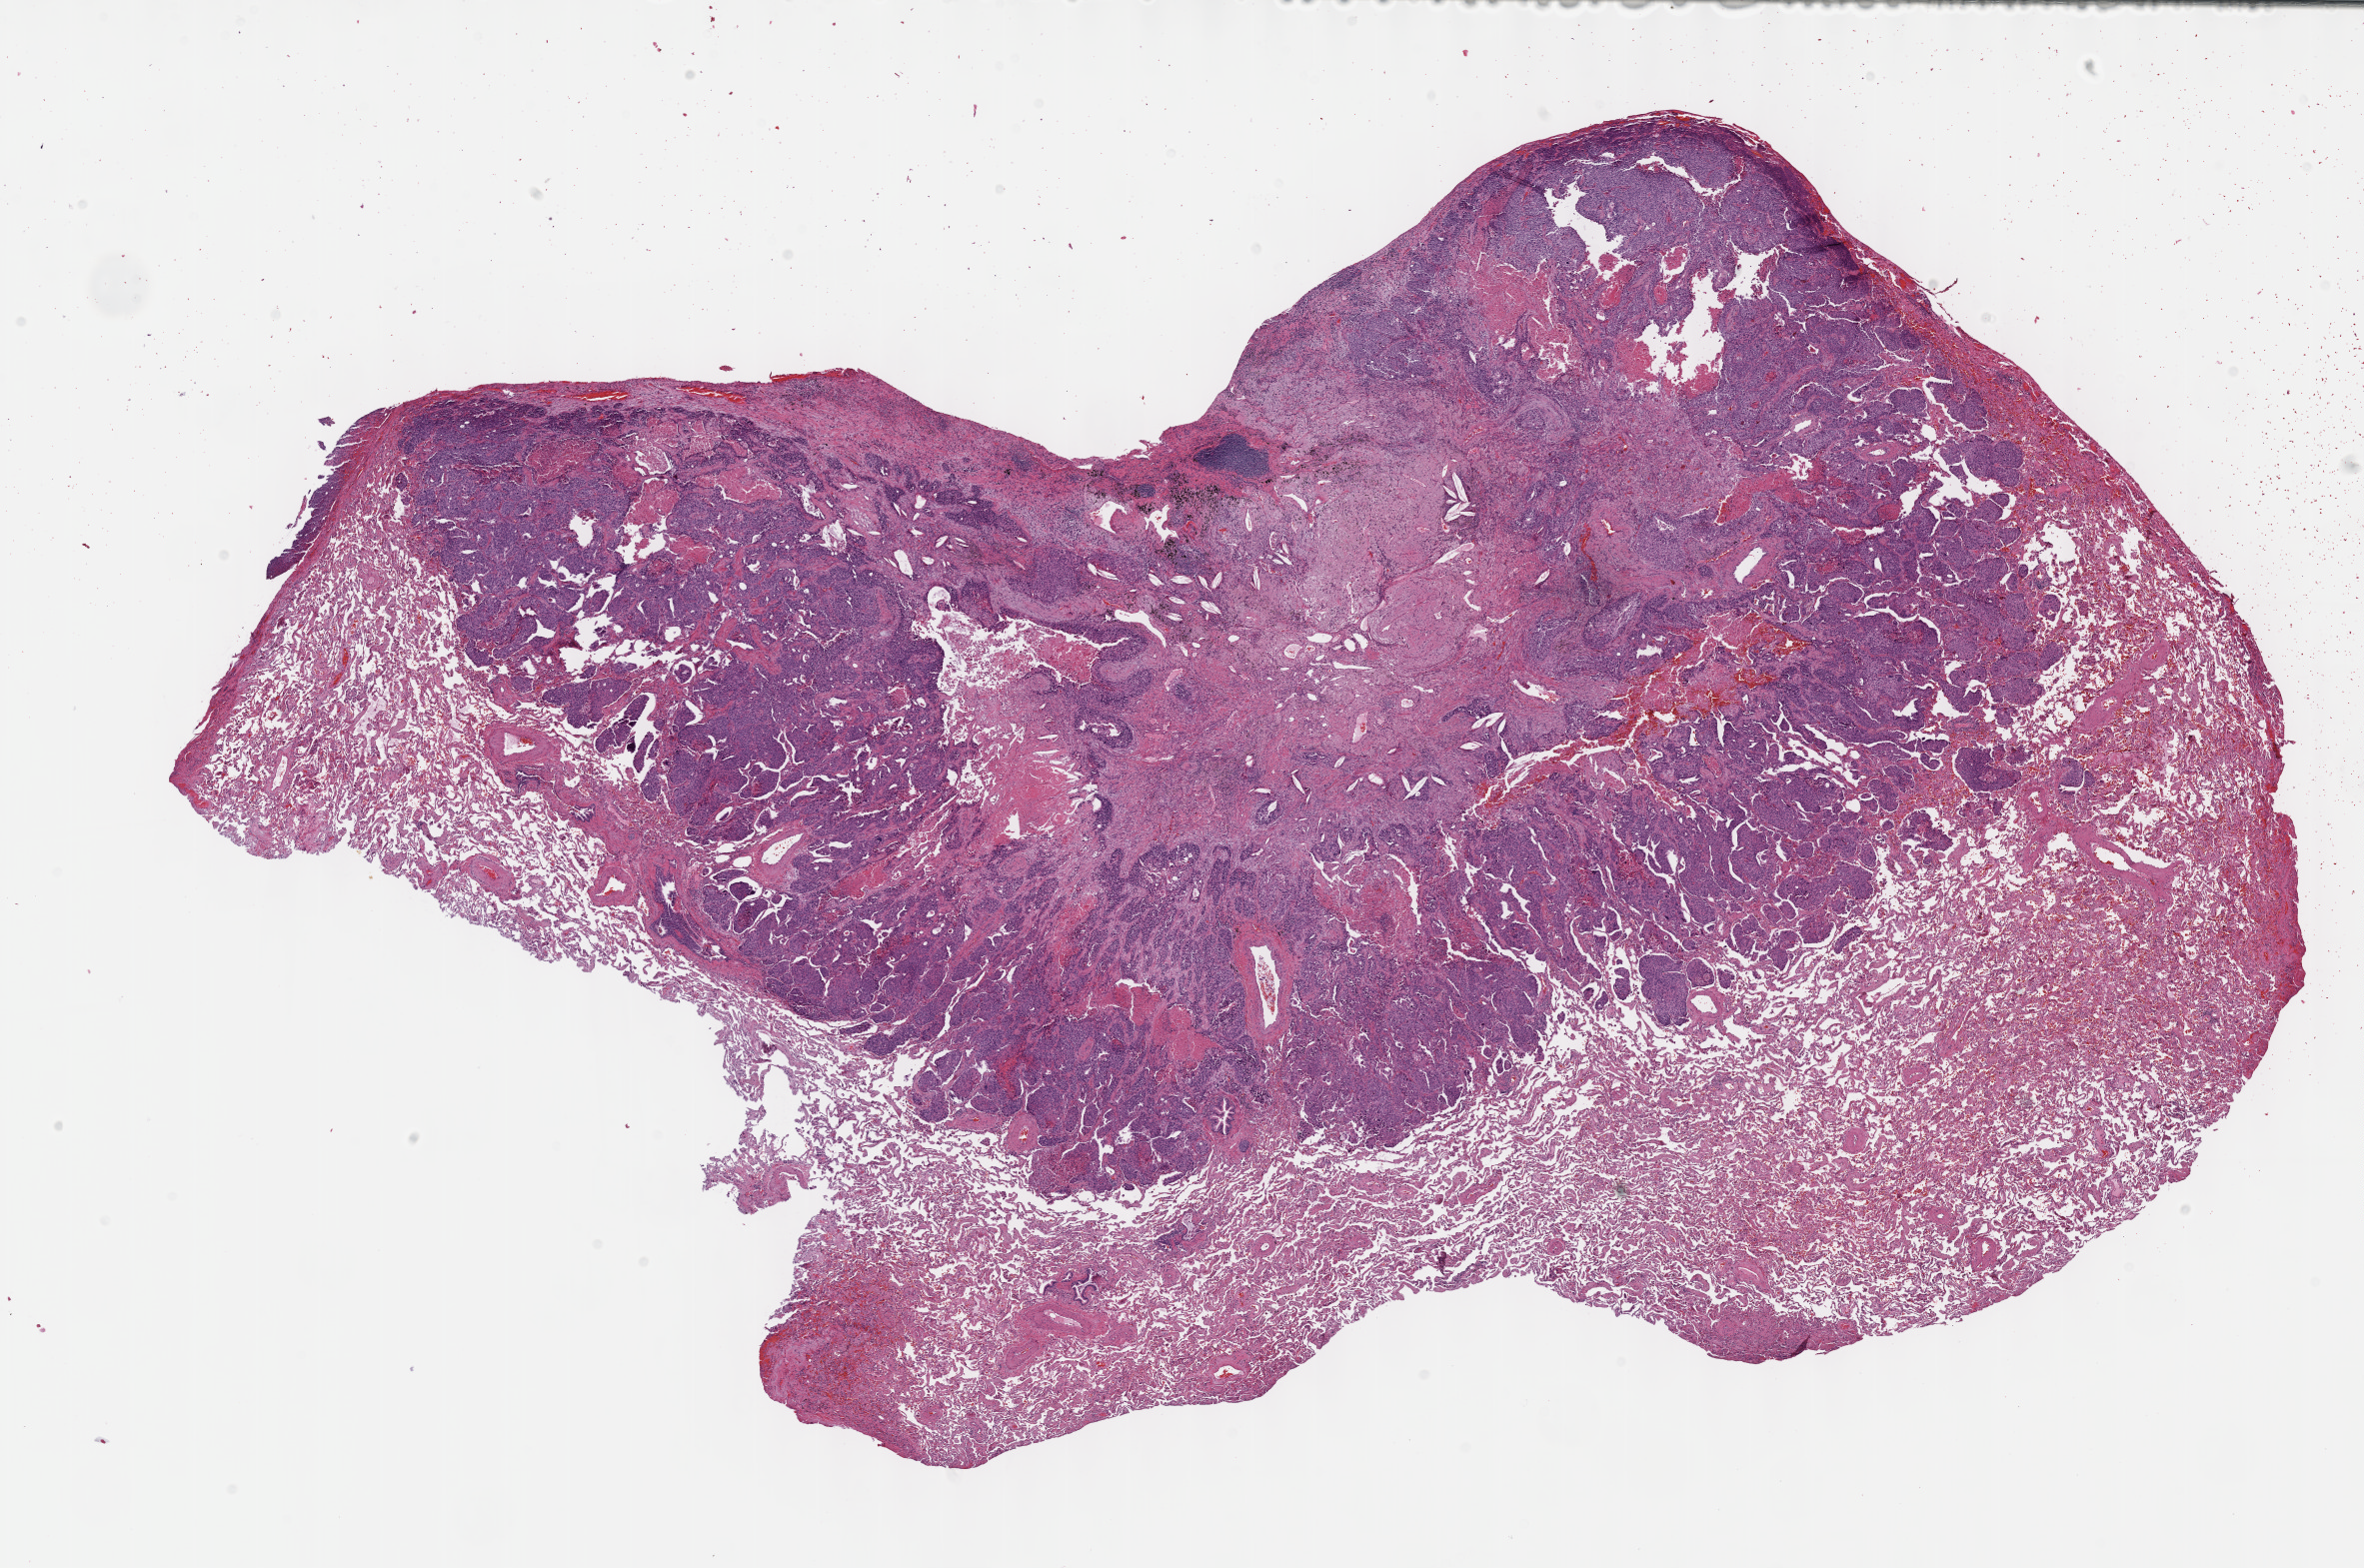
H&E whole-slide image, whole scanned area (about 19.1 x 12.7 mm) shown as a low-resolution overview, formalin-fixed paraffin-embedded (FFPE) diagnostic section, sample: primary tumour, lung. Female, age 73 years at initial diagnosis.
* histologic diagnosis: Squamous cell carcinoma, NOS (upper lobe, lung)
* AJCC pathologic stage: IIIA
* laterality: right